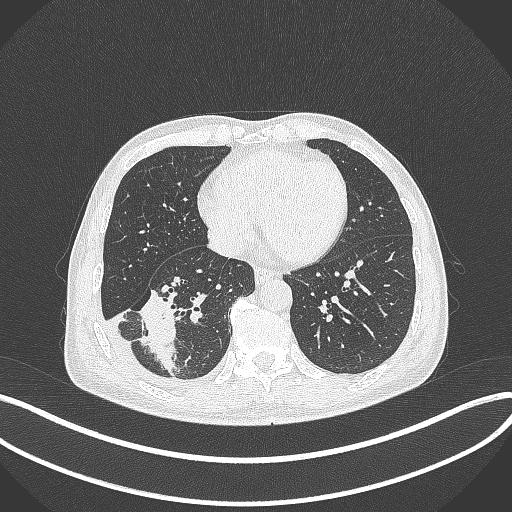
Chest CT, one axial slice; position 132 of 388 along the scan axis; 120 kVp; lung window (W 1500 / L -600 HU); 1 mm slice thickness; 512 × 512 image matrix, field of view 400 × 400 mm. Male patient, age 64 years. From the clinical record (not read from this slice): clinical TNM (as recorded): T3 N0 M0.
Outlined on this slice (rectangle marked by the reading radiologist):
- lung tumour (recorded histology: adenocarcinoma): box from (x=130, y=289) to (x=183, y=382) px